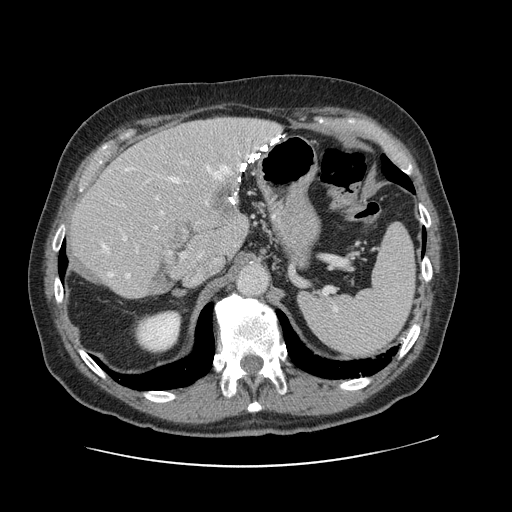
Contrast-enhanced abdominal CT, one axial slice; slice 79 of 138 in the series (ordered by position); 120 kVp; intravenous contrast given; soft-tissue window (W 400 / L 40 HU); 2.5 mm slice thickness; 512 × 512 image matrix, field of view 402 × 402 mm. Male patient, age 71 years. From the clinical record (not read from this slice): diagnosis: colorectal cancer liver metastases, imaged before liver resection; multiple liver metastases: no; largest metastasis: 3.3 cm.
Annotated regions visible in this slice (expert manual segmentation):
- hepatic veins: bounding box <101,147,257,278> (left, top, right, bottom; pixels)
- liver: <70,118,279,298>
- planned liver remnant (the part of the liver to remain after resection): <70,150,236,298>
- portal vein (with intrahepatic branches): <122,161,188,258>
- liver metastasis: <207,183,236,219>